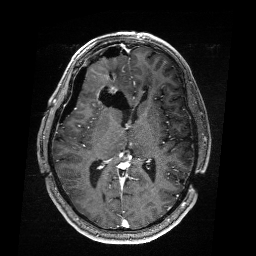
Brain MRI from a brain-tumour surgery series, one axial slice. Slice 102 of 176 in the series (ordered by position). T1-weighted post-contrast. 1 mm slice thickness. 256 × 256 image matrix. From the clinical record (not read from this slice): histopathology: Astrocytoma; WHO grade: 4; IDH mutation: yes.
Outlined on this slice (expert manual segmentation):
- residual tumour: bounding box (x1, y1, x2, y2) in pixels: (96, 82, 116, 91)